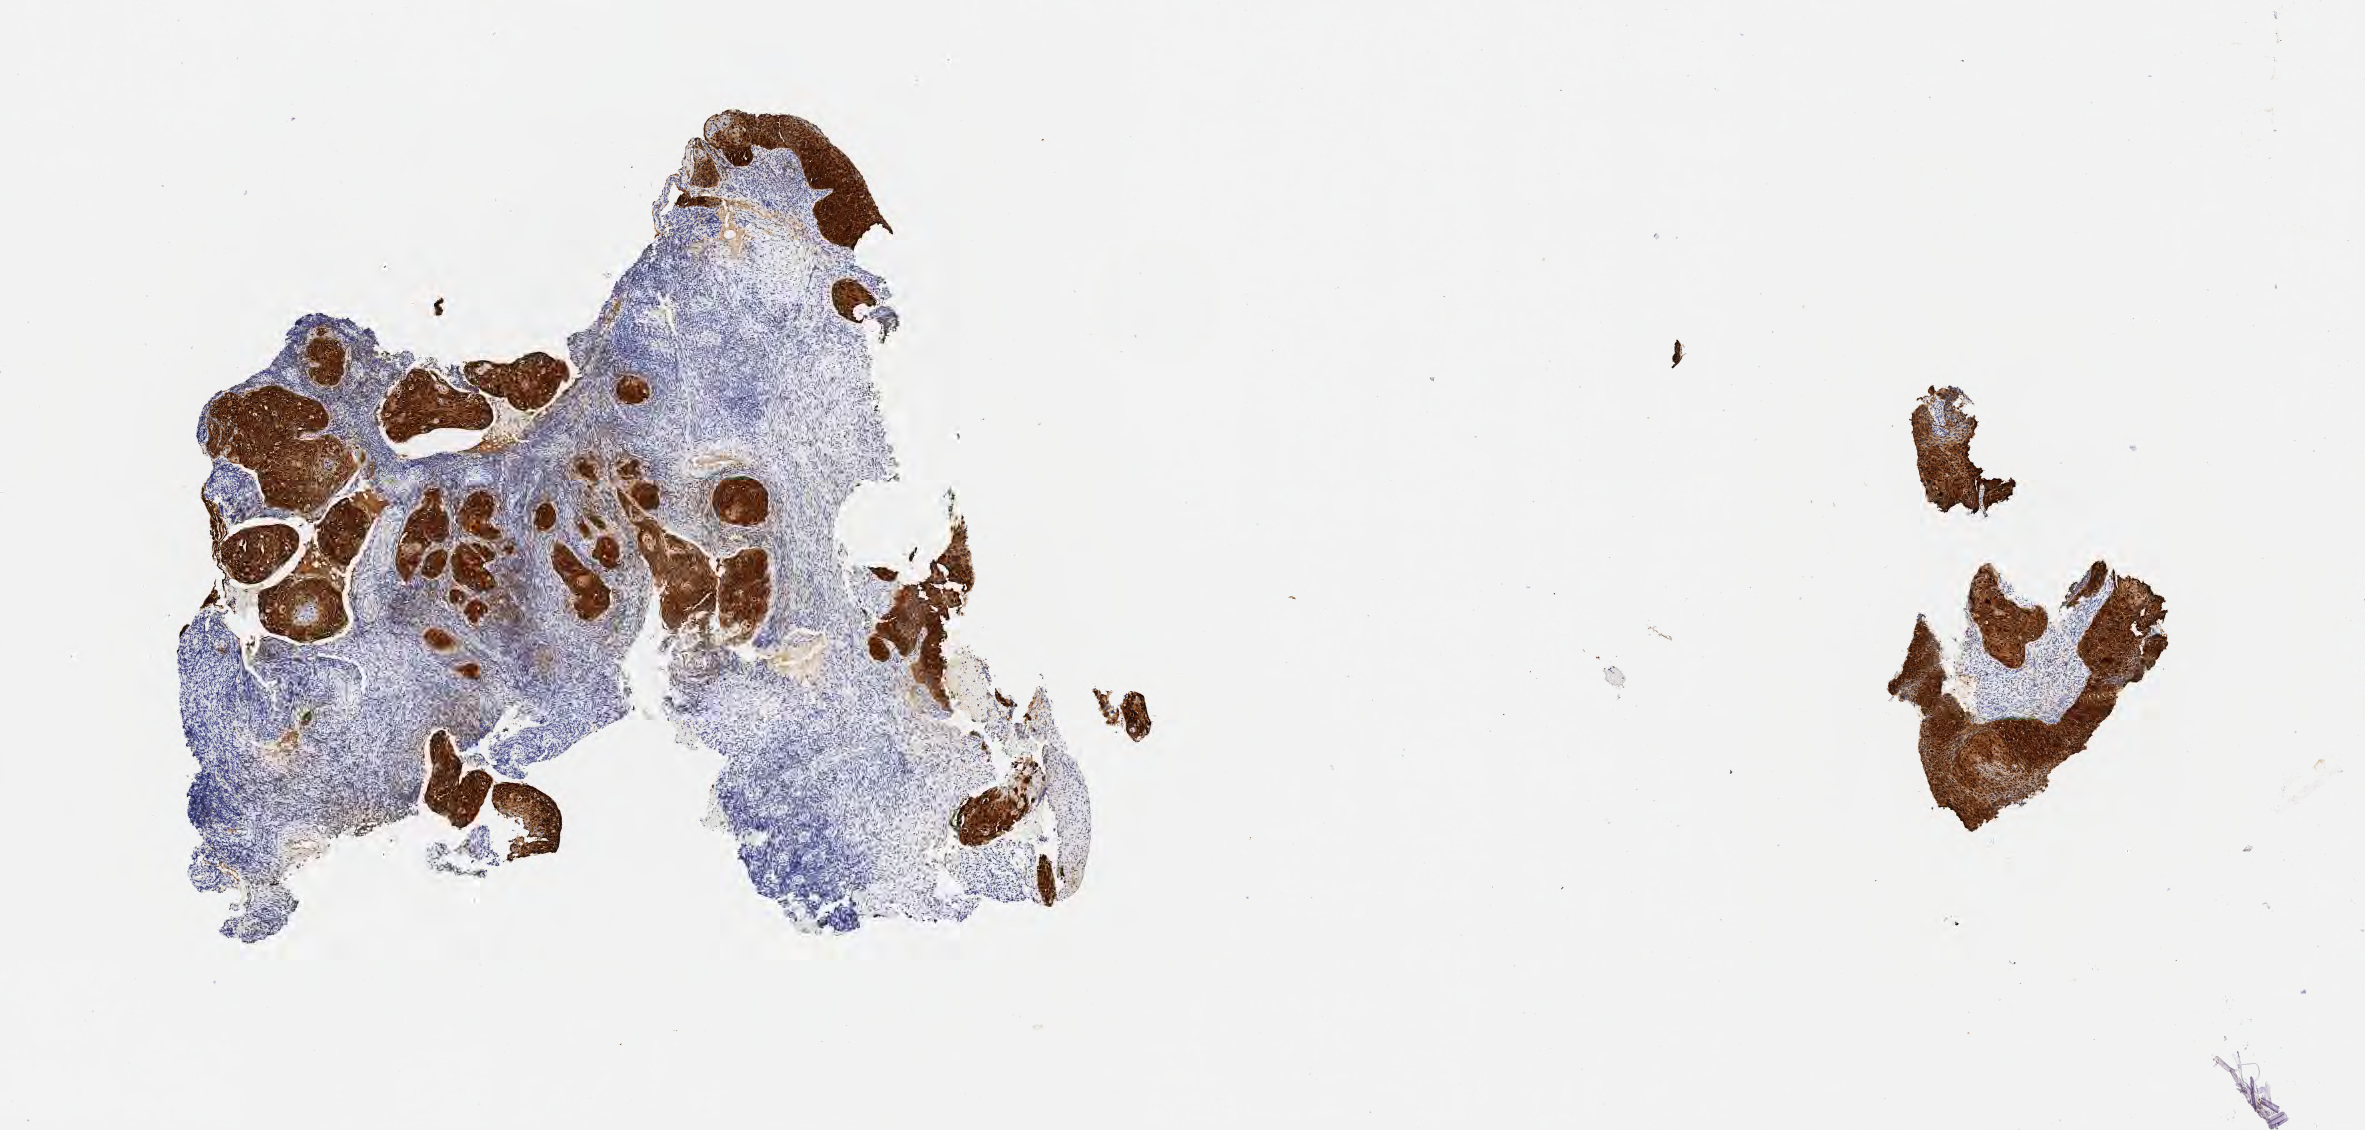
Immunohistochemistry (IHC) whole-slide image stained for p16 (p16INK4a) — whole scanned area (about 9.6 x 4.6 mm) shown as a low-resolution overview, specimen: tumor tissue, anatomic site: cervix. Patient: female, 40 years old.
Diagnosis: Squamous cell carcinoma, keratinizing, NOS.